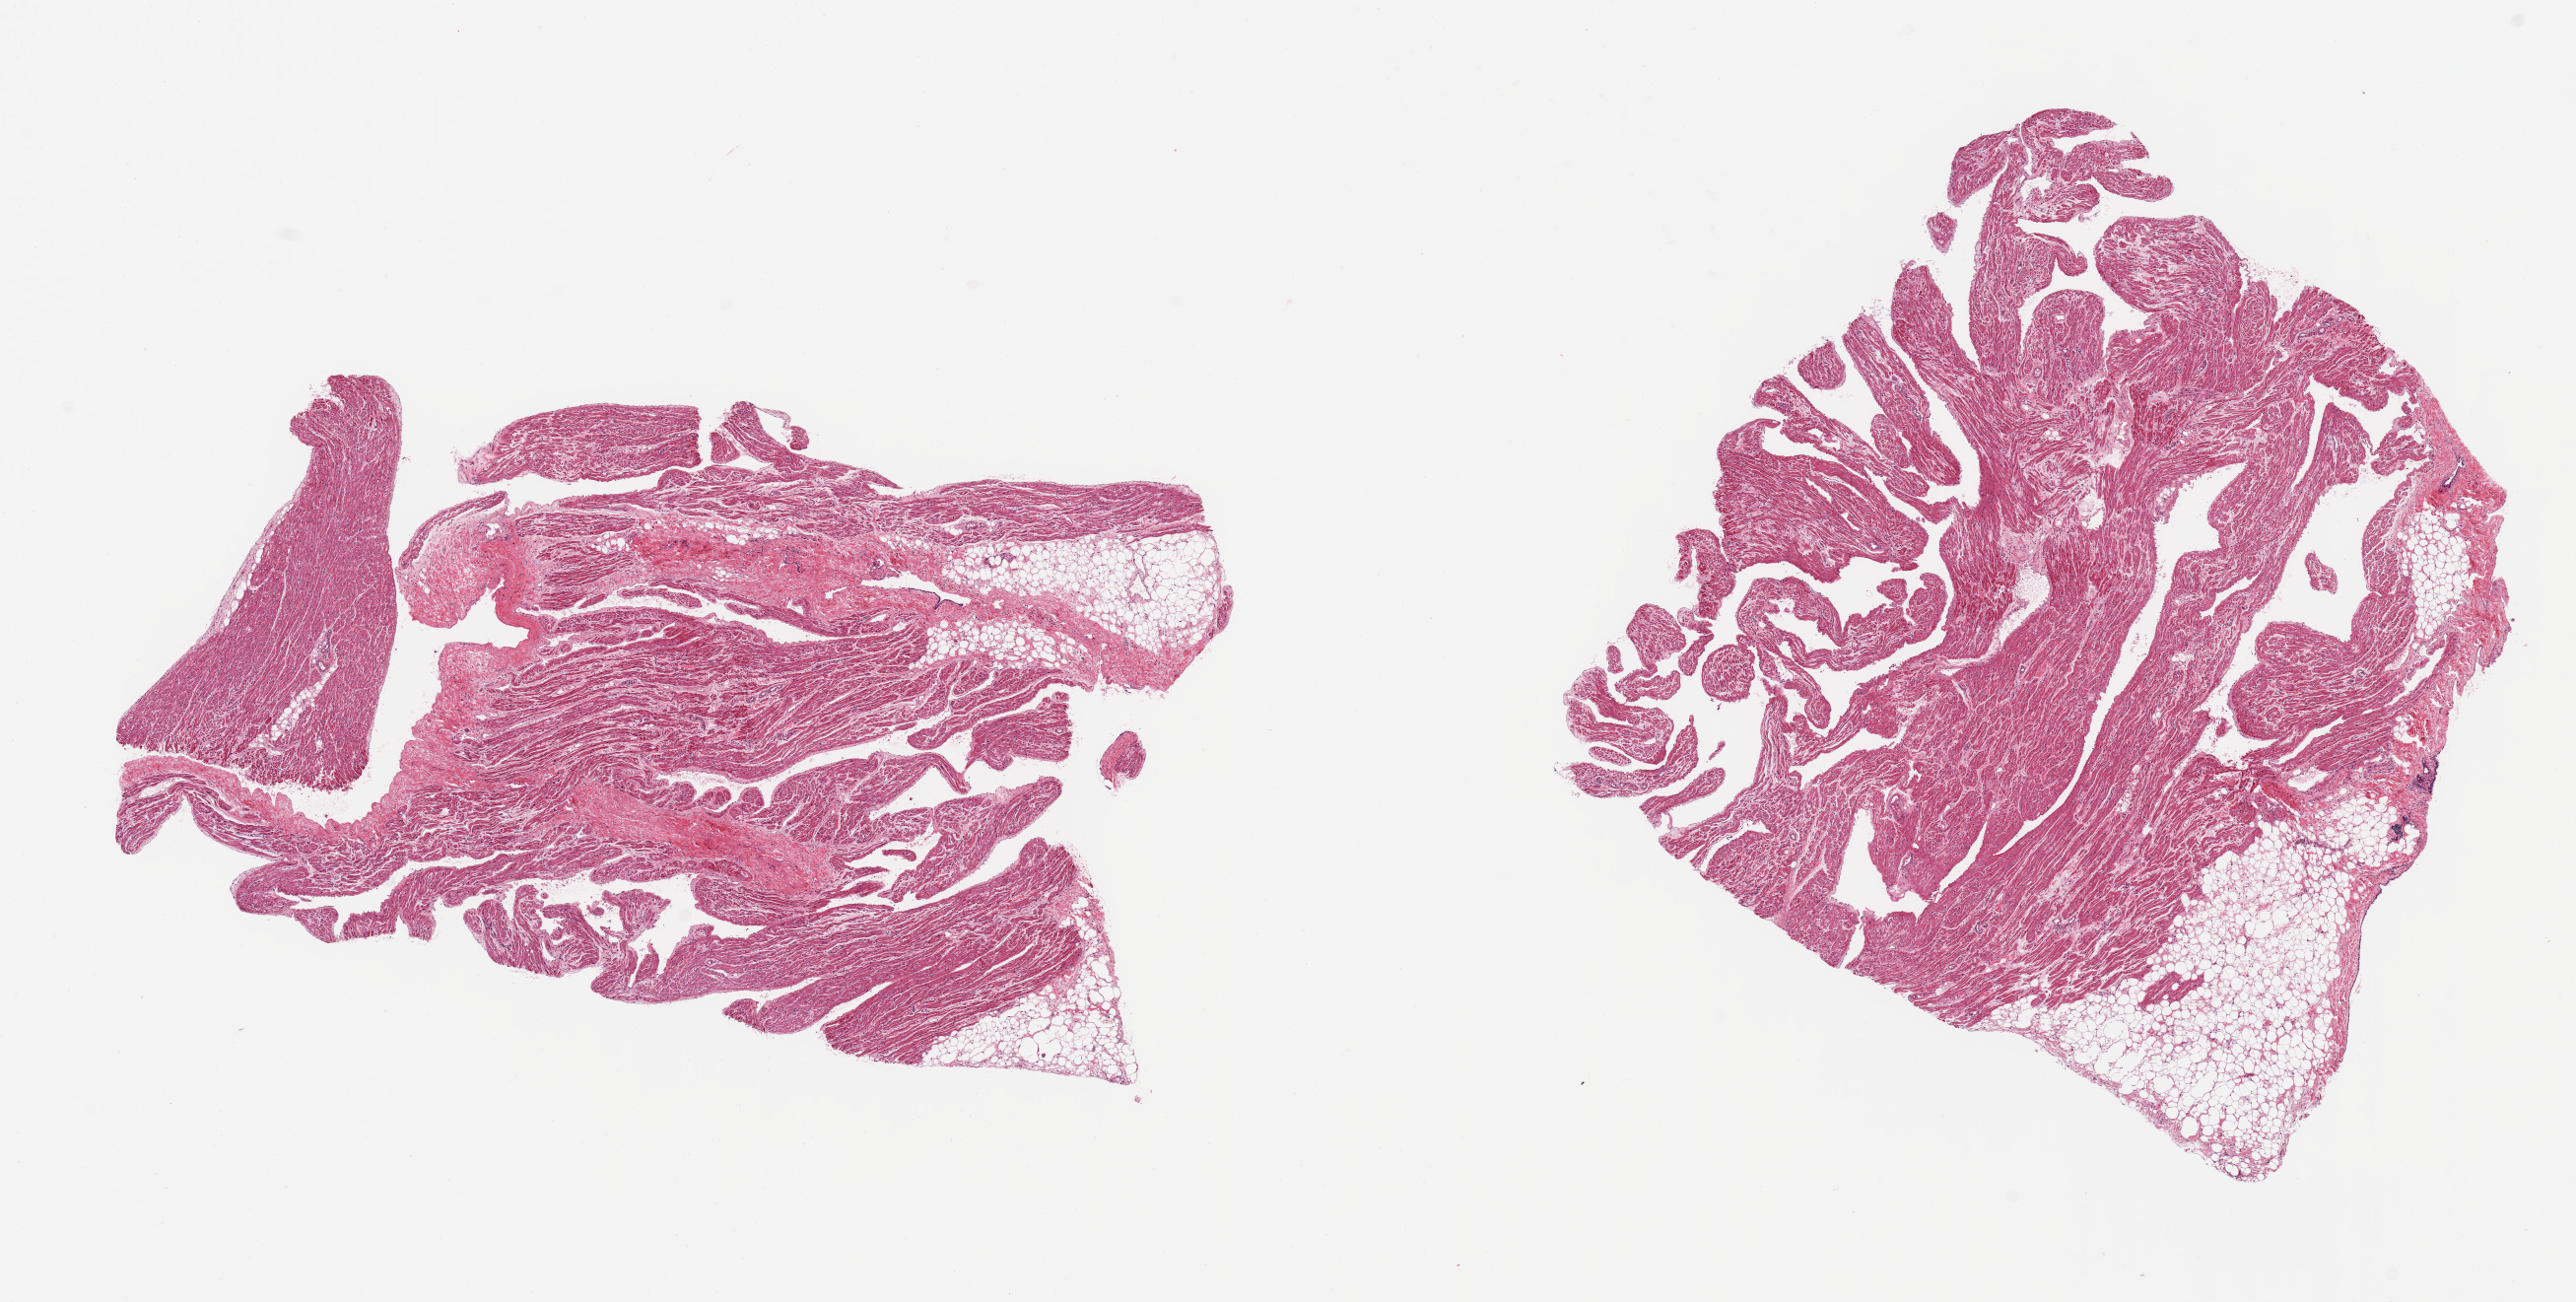
Whole-slide image, haematoxylin and eosin stain — whole scanned area (about 20.7 x 10.4 mm) shown as a low-resolution overview; PAXgene-fixed, paraffin-embedded tissue; section of auricular appendage (target tissue); donor tissue sample.
Pathologist's review note for this sample: 2 pieces; 20% external fat.